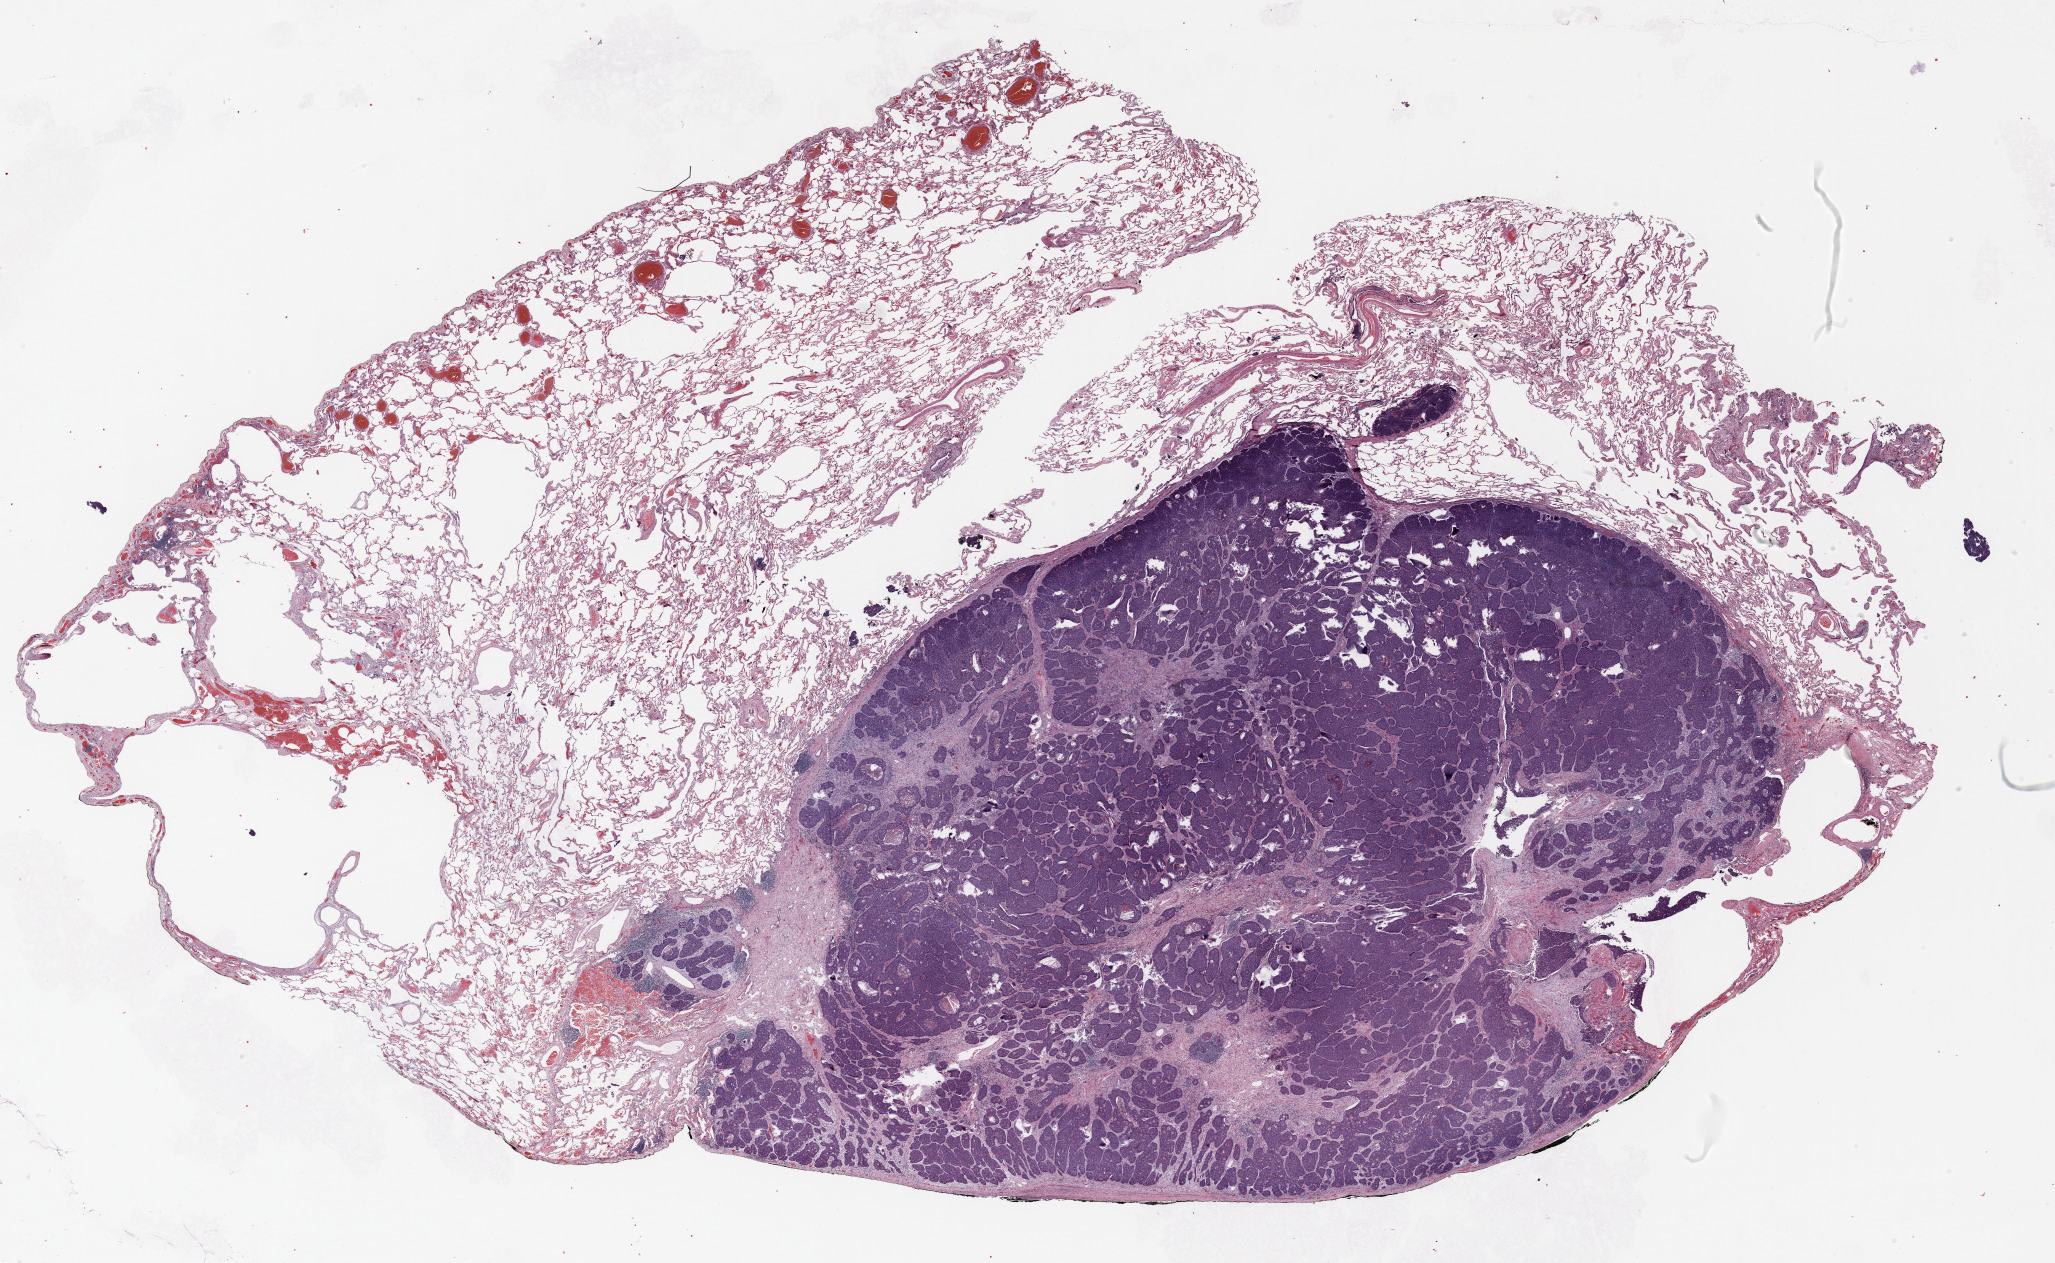
Whole-slide histology image, H&E-stained, shown as a low-resolution overview of the whole scanned area (about 33.0 x 20.3 mm, from a 20x scan); formalin-fixed paraffin-embedded (FFPE) section; lung tissue. Female, age 74 at enrolment. Grade: poorly differentiated (G3).
Tumour size (pathology): 24 mm. Stage (AJCC 6th edition): IA. Primary tumour location (clinical record): left upper lobe. Participant's lung-cancer diagnosis: Adenocarcinoma, NOS (ICD-O-3 8140/3).